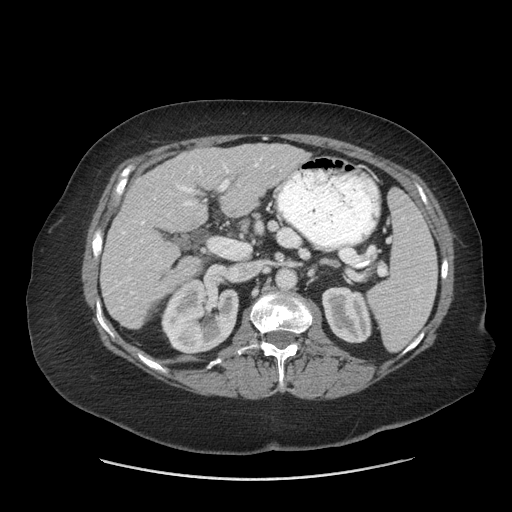
Contrast-enhanced abdominal CT (liver protocol), one axial slice; slice 31 of 69 in the series (ordered by position); reconstruction kernel STANDARD; 140 kVp; soft-tissue window (W 400 / L 40 HU); 2.5 mm slice thickness; 512 × 512 image matrix. Case-level facts recorded for this patient, not image findings: diagnosis: hepatocellular carcinoma (patient treated with transarterial chemoembolisation; whether this scan precedes or follows treatment is not stated here); TNM stage (as recorded): Stage-IIIB; Child-Pugh class: A; tumour nodularity: multinodular.
Annotated regions visible in this slice (semi-automatic segmentation, software-assisted and operator-edited):
- liver parenchyma outside the tumour (the mass and vessels are separate outlines, so this box may not span the whole liver): bounding box <100,144,309,328> (left, top, right, bottom; pixels)
- liver vessels: <119,158,274,309>